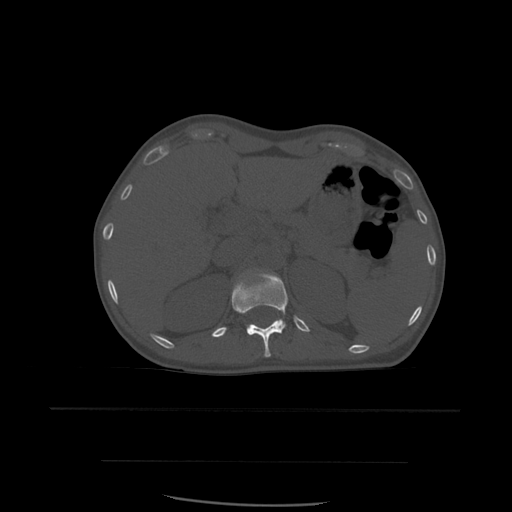
CT including the spine, one axial slice. Slice 271 of 574 in the series (ordered by position). Bone window (W 1800 / L 400 HU). 512 × 512 image matrix, field of view 392 × 392 mm. Patient age 48 years. Case-level facts recorded for this patient, not image findings: primary cancer: lung.
Outlined on this slice (semi-automatic segmentation, software-assisted and operator-edited):
- T12 vertebra: bounding box (x1, y1, x2, y2) in pixels: (232, 272, 289, 358)